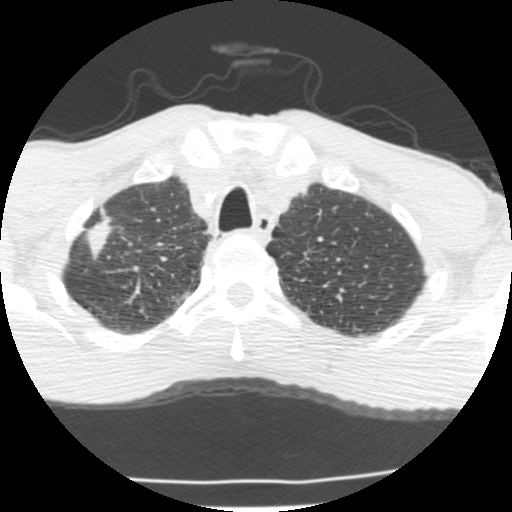
Low-dose screening chest CT, one axial slice. Position 181 of 214 along the scan axis. Reconstruction kernel STANDARD. Lung window (W 1500 / L -600 HU). 2.5 mm slice thickness. 512 × 512 image matrix, field of view 283 × 283 mm.
Outlined on this slice (expert manual segmentation):
- lesion 1 (tumor, upper lobe of right lung): bounding box <84,209,114,260> (left, top, right, bottom; pixels)